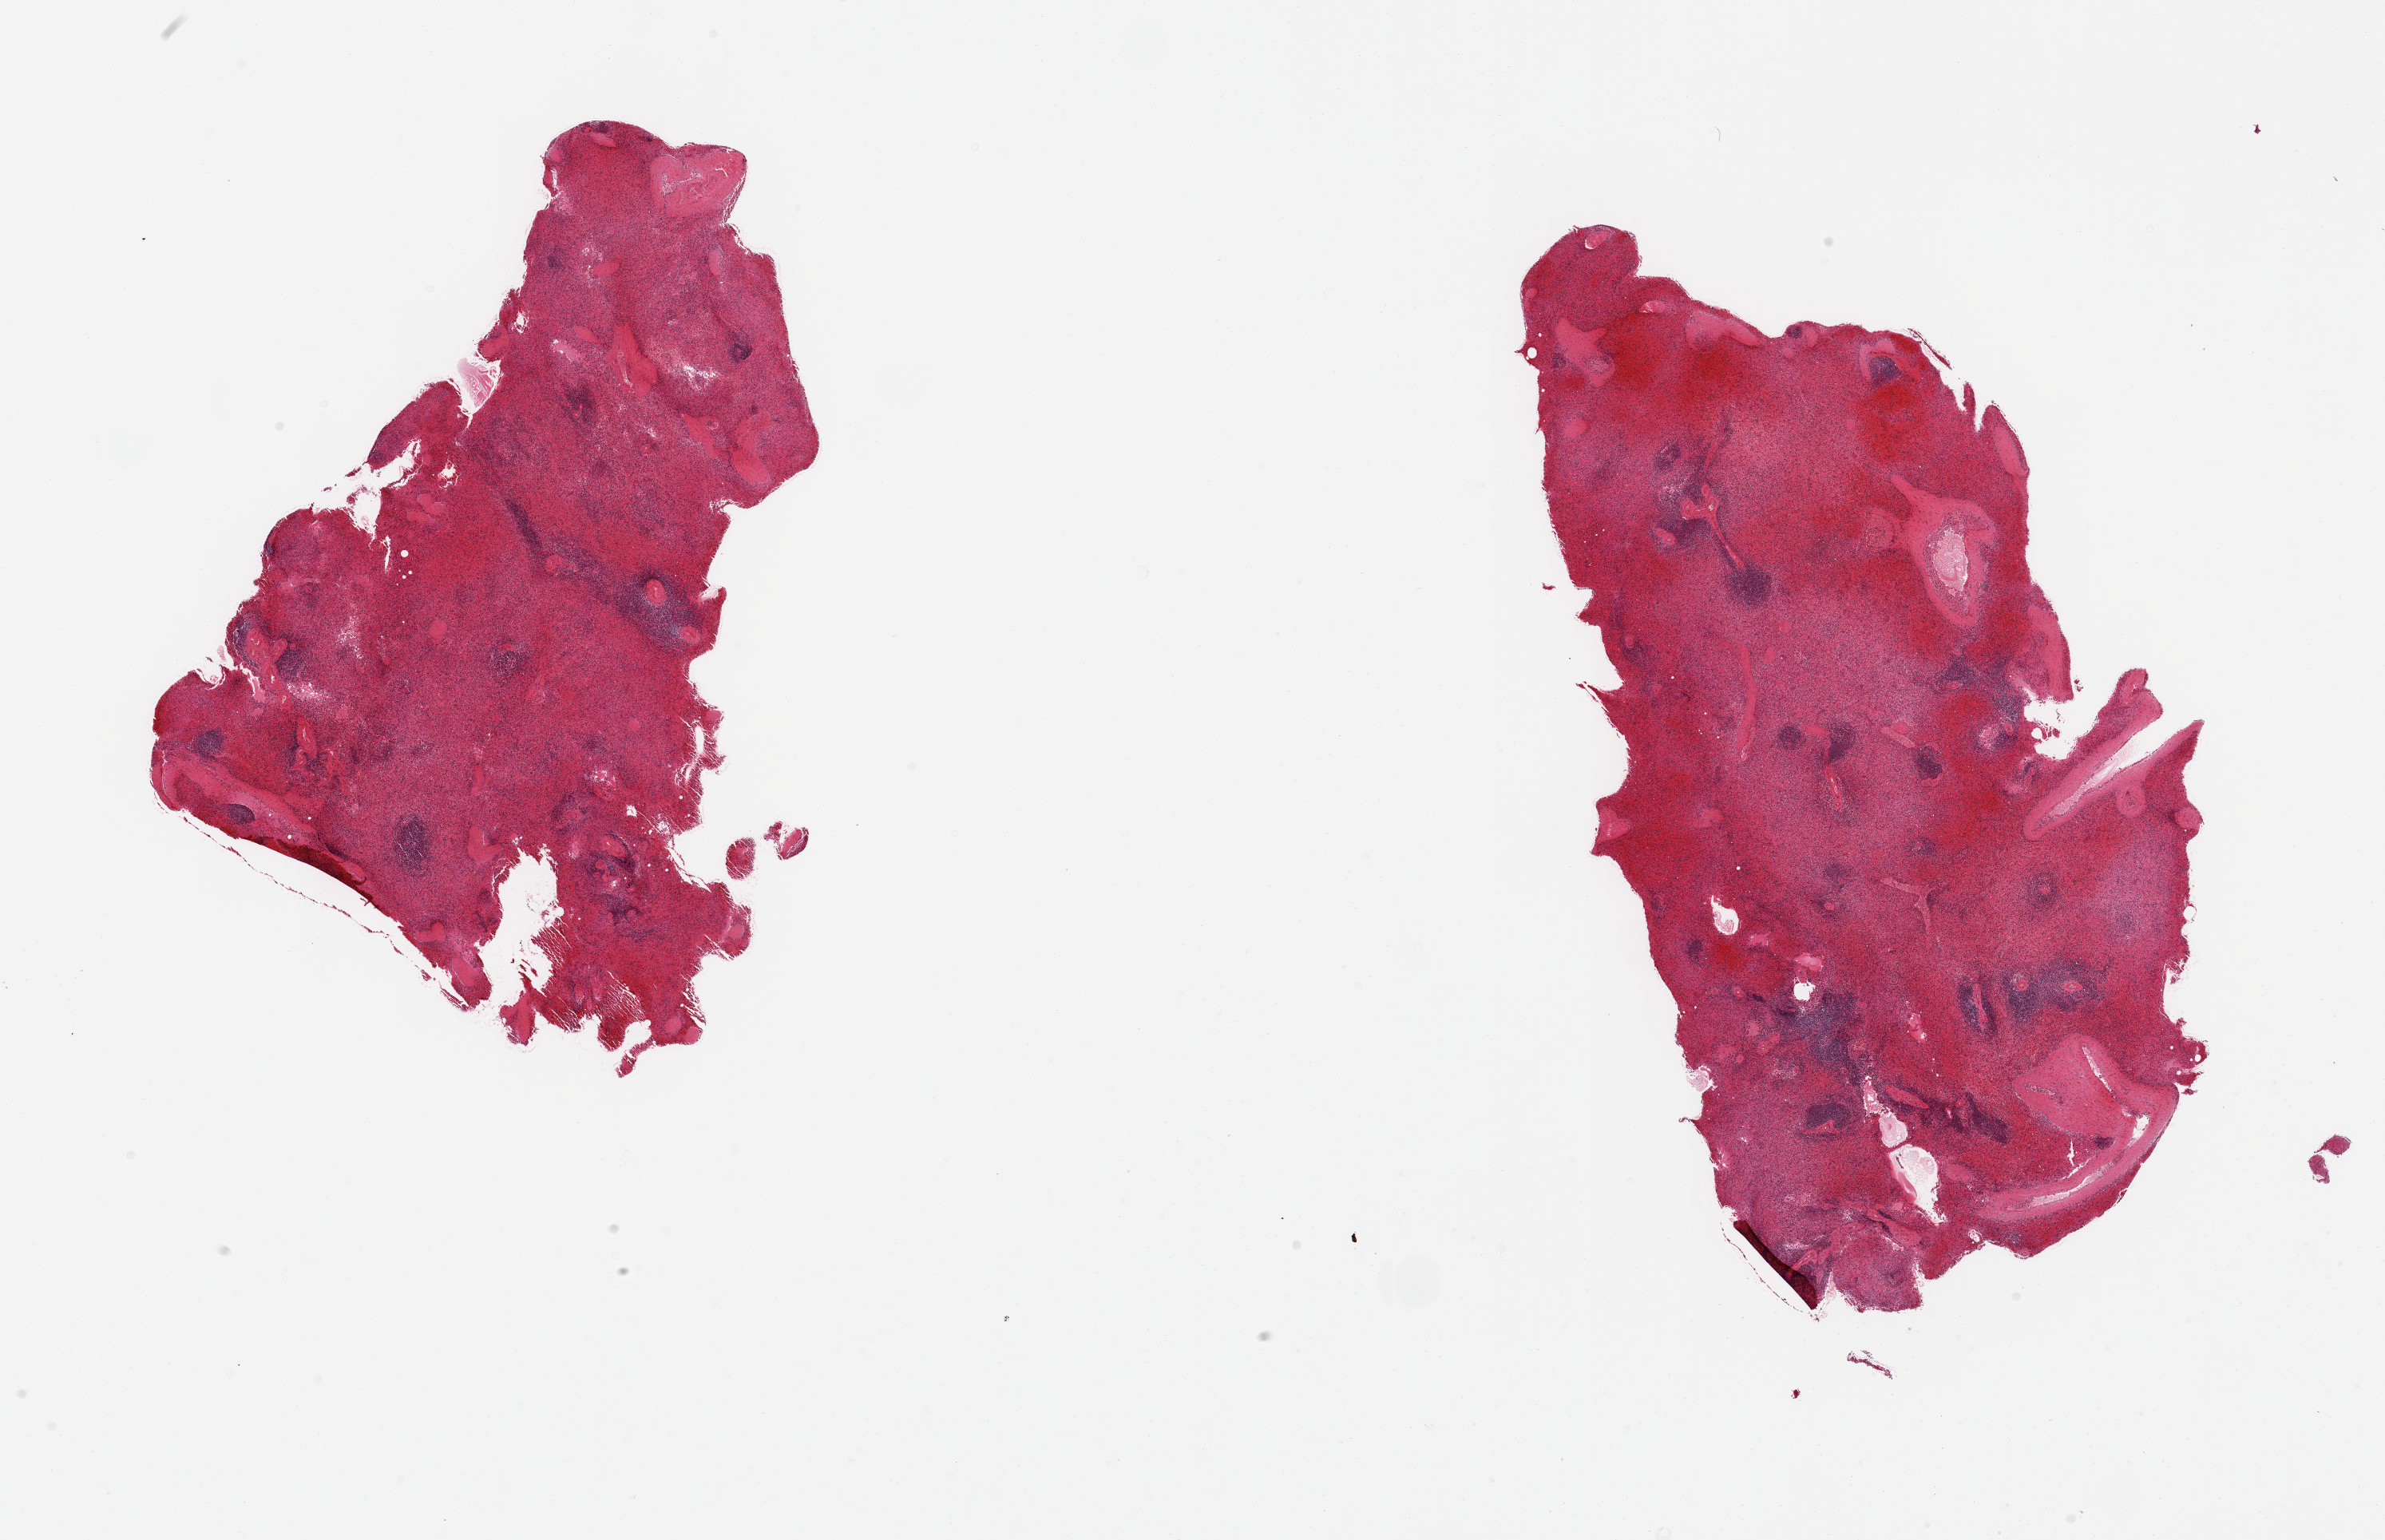
Whole-slide image, hematoxylin and eosin (H&E) stain — whole scanned area (about 23.6 x 15.3 mm) shown as a low-resolution overview; PAXgene-fixed paraffin-embedded (PFPE) section; sampled site (target tissue): spleen; tissue donor sample.
Review note (as recorded): 2 pieces; marked congestion.